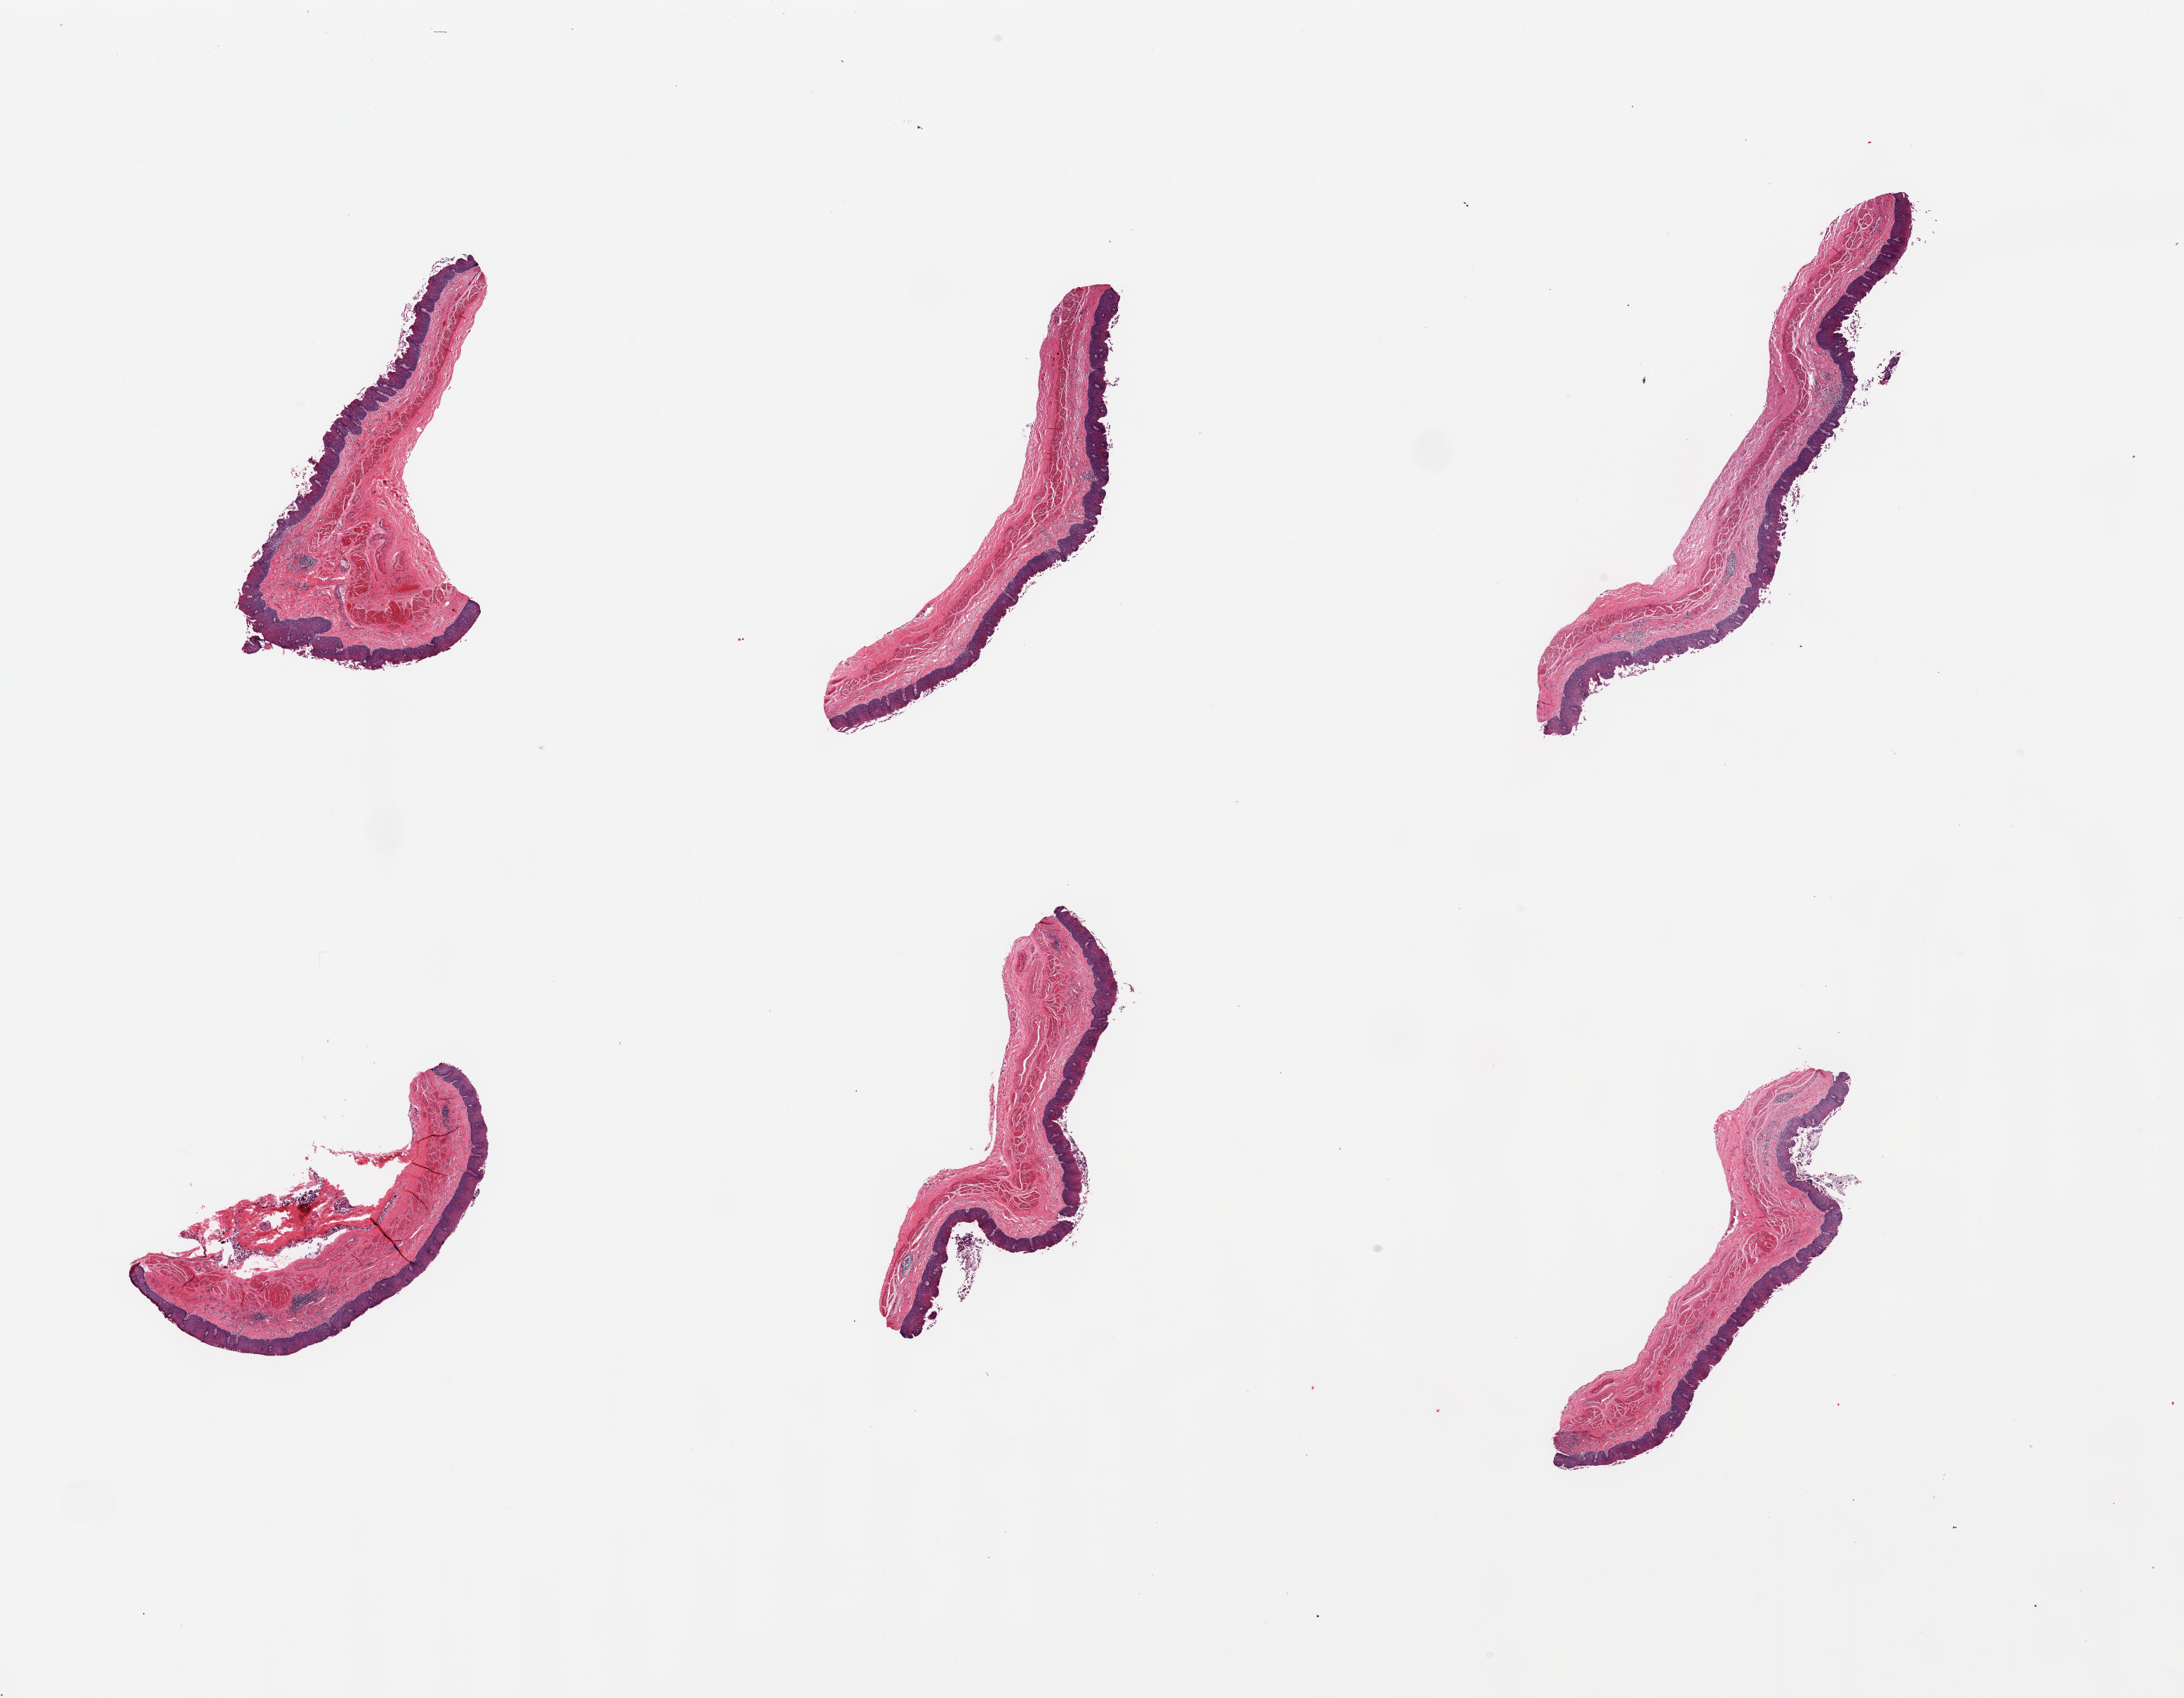
Digitized H&E-stained section, brightfield, a low-resolution overview of the entire scanned area, about 24.6 x 19.1 mm (slide scanned at 20x). PAXgene-fixed, paraffin-embedded tissue. Sampled site (target tissue): esophageal mucous membrane. Tissue donor sample. Donor sex: female.
* review note (as recorded): 6 pieces; chronic inflammation; partially sloughed epithelium; focus of carry-over debris on deep surface of 1 piece